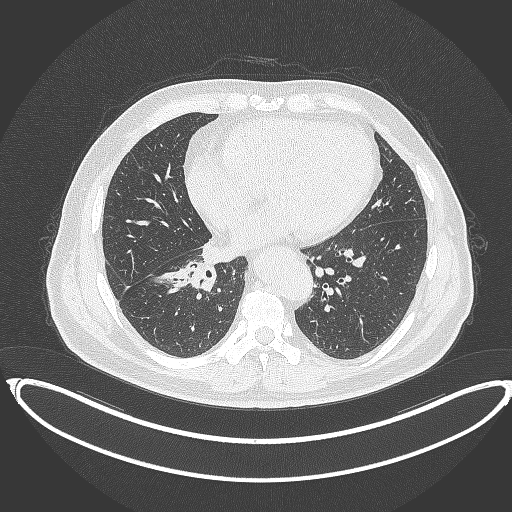
Chest CT, one axial slice; slice 162 of 387 in the series (ordered by position); reconstruction kernel B70f; 120 kVp; lung window (W 1500 / L -600 HU); 1 mm slice thickness; 512 × 512 image matrix. Patient: male, 61 years. Case-level facts recorded for this patient, not image findings: clinical TNM (as recorded): T1b N1 M0.
Annotated regions visible in this slice (bounding box drawn by a radiologist):
- lung tumour (recorded histology: squamous cell carcinoma): box from (x=181, y=257) to (x=218, y=291) px